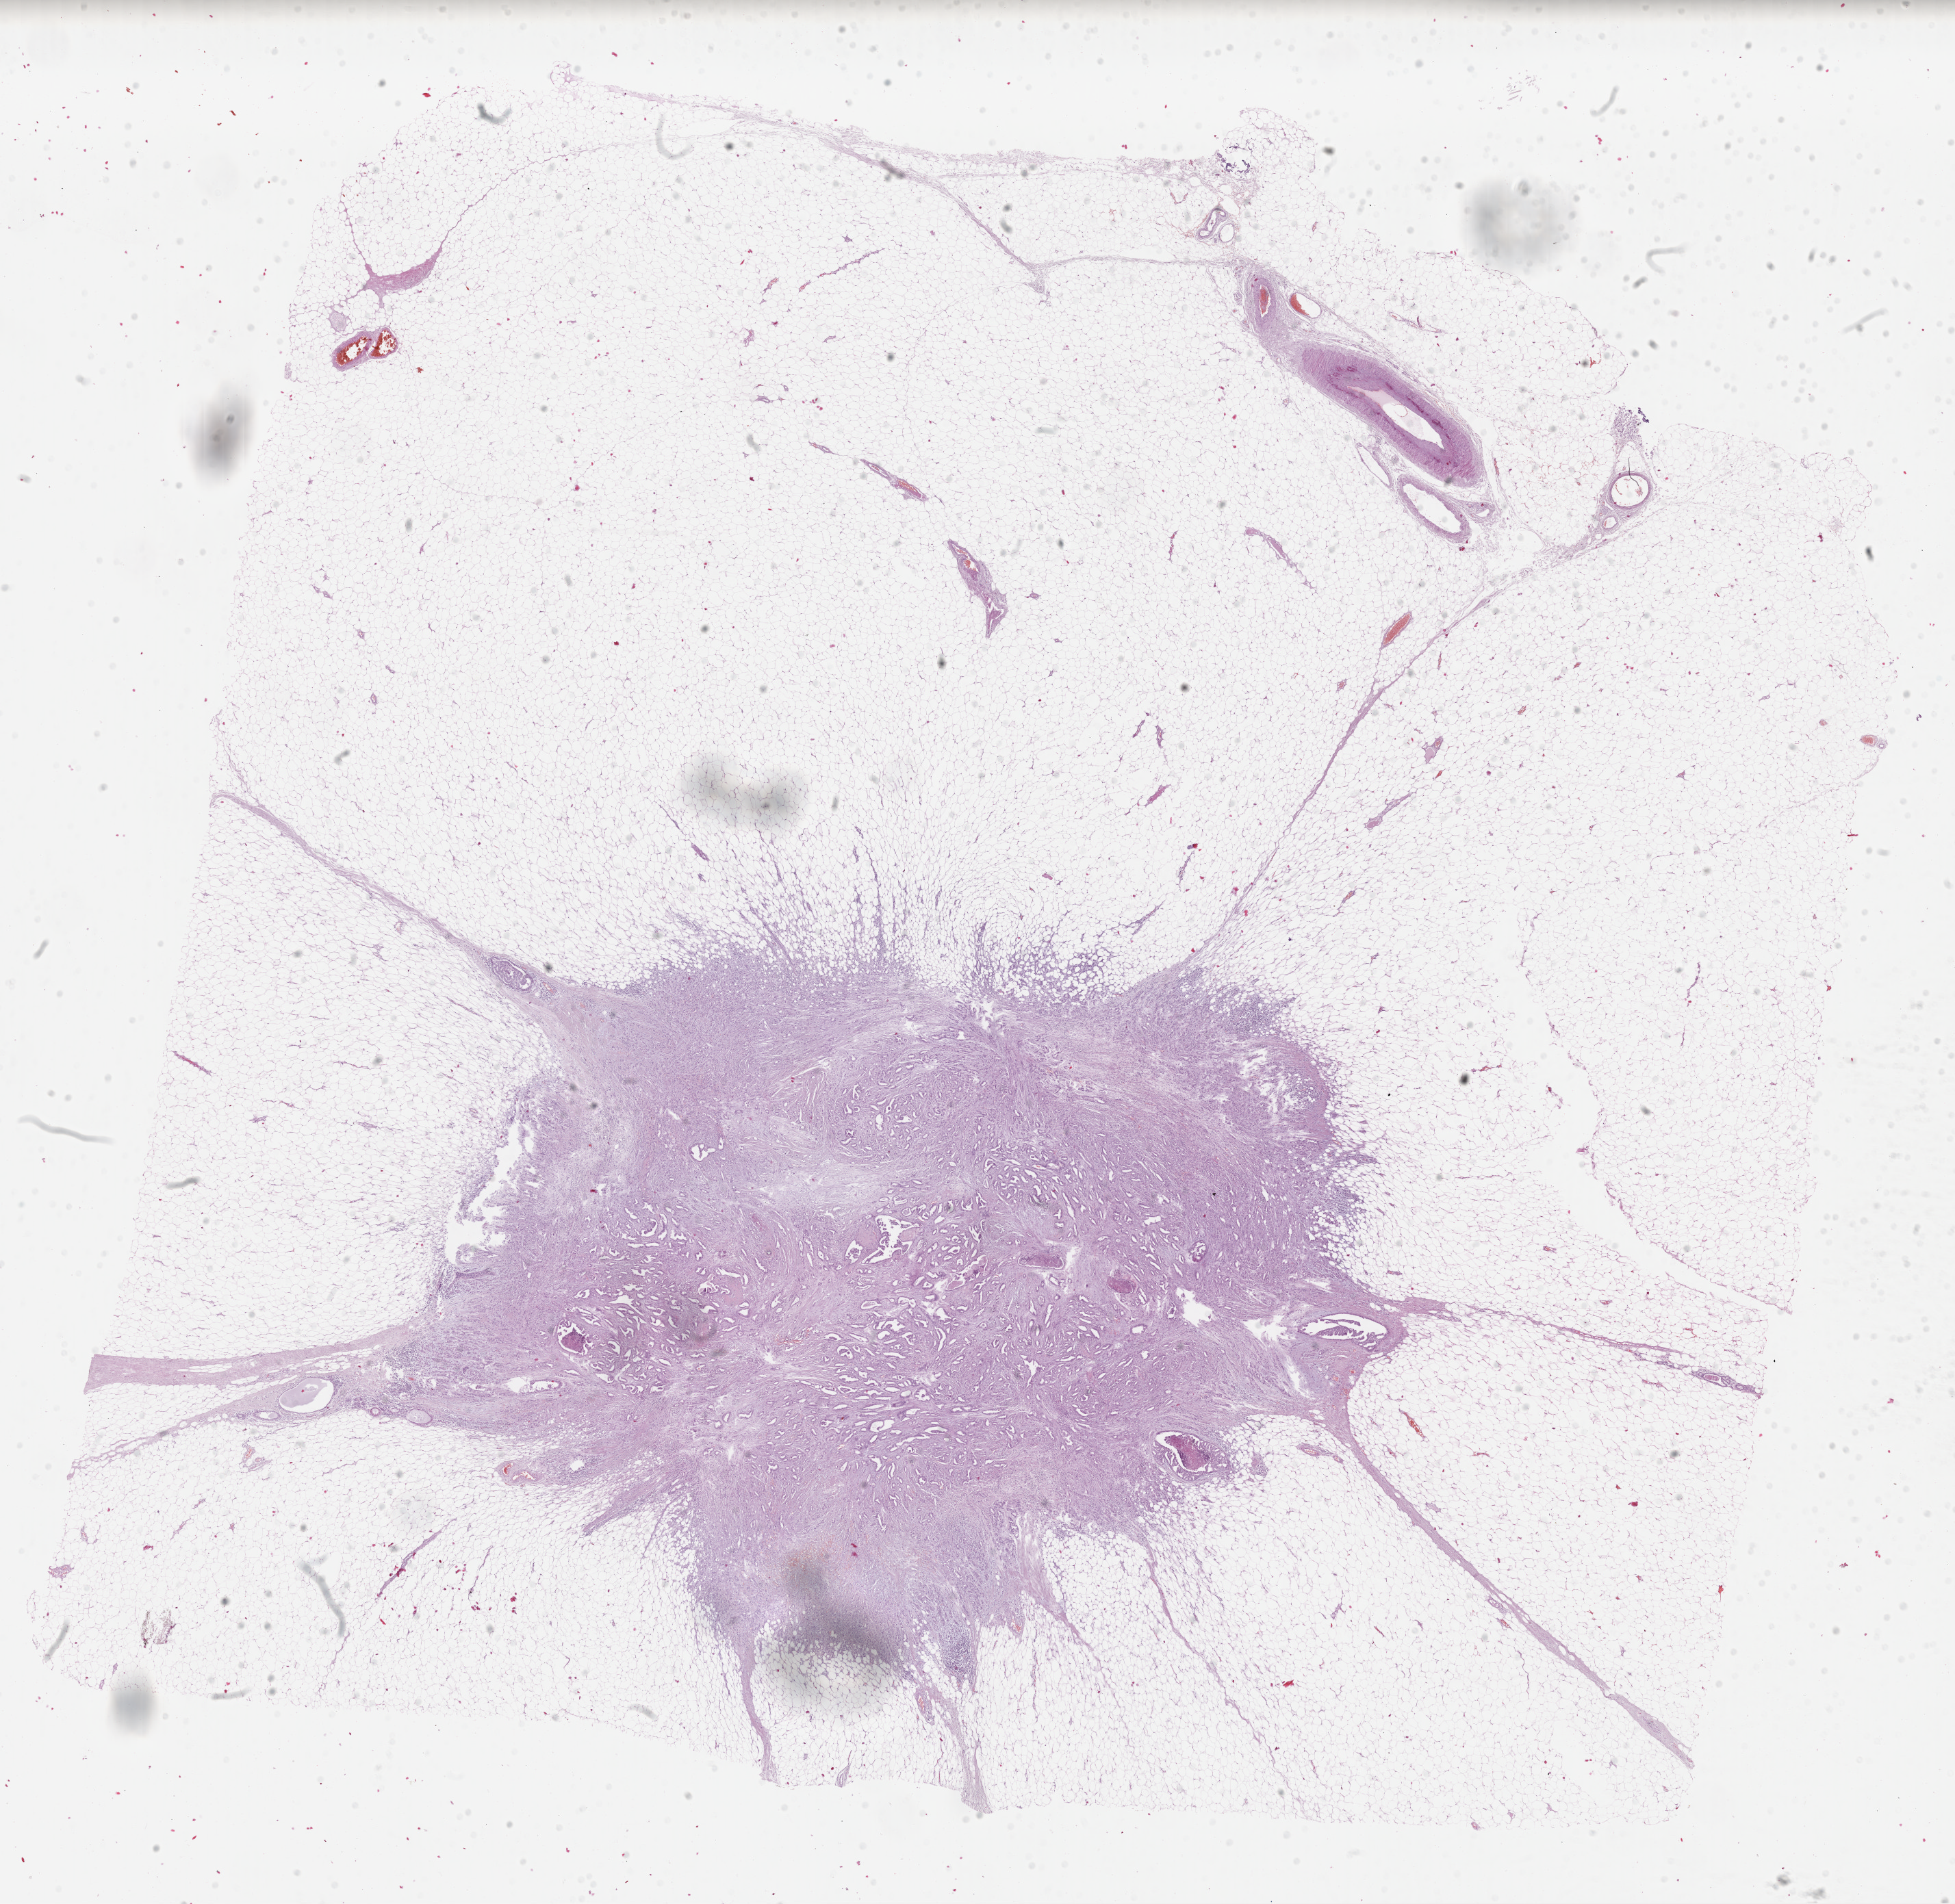
H&E whole-slide image — shown as a low-resolution overview of the whole scanned area (about 22.6 x 22.0 mm, from a 40x scan), formalin-fixed paraffin-embedded (FFPE) diagnostic section, sample: primary tumour, breast. Patient: female, age at initial diagnosis 57 years.
• pathologic diagnosis: Infiltrating duct carcinoma, NOS
• lymph nodes positive (case pathology): 0 of 1 examined
• AJCC pathologic stage: IA (7th edition)